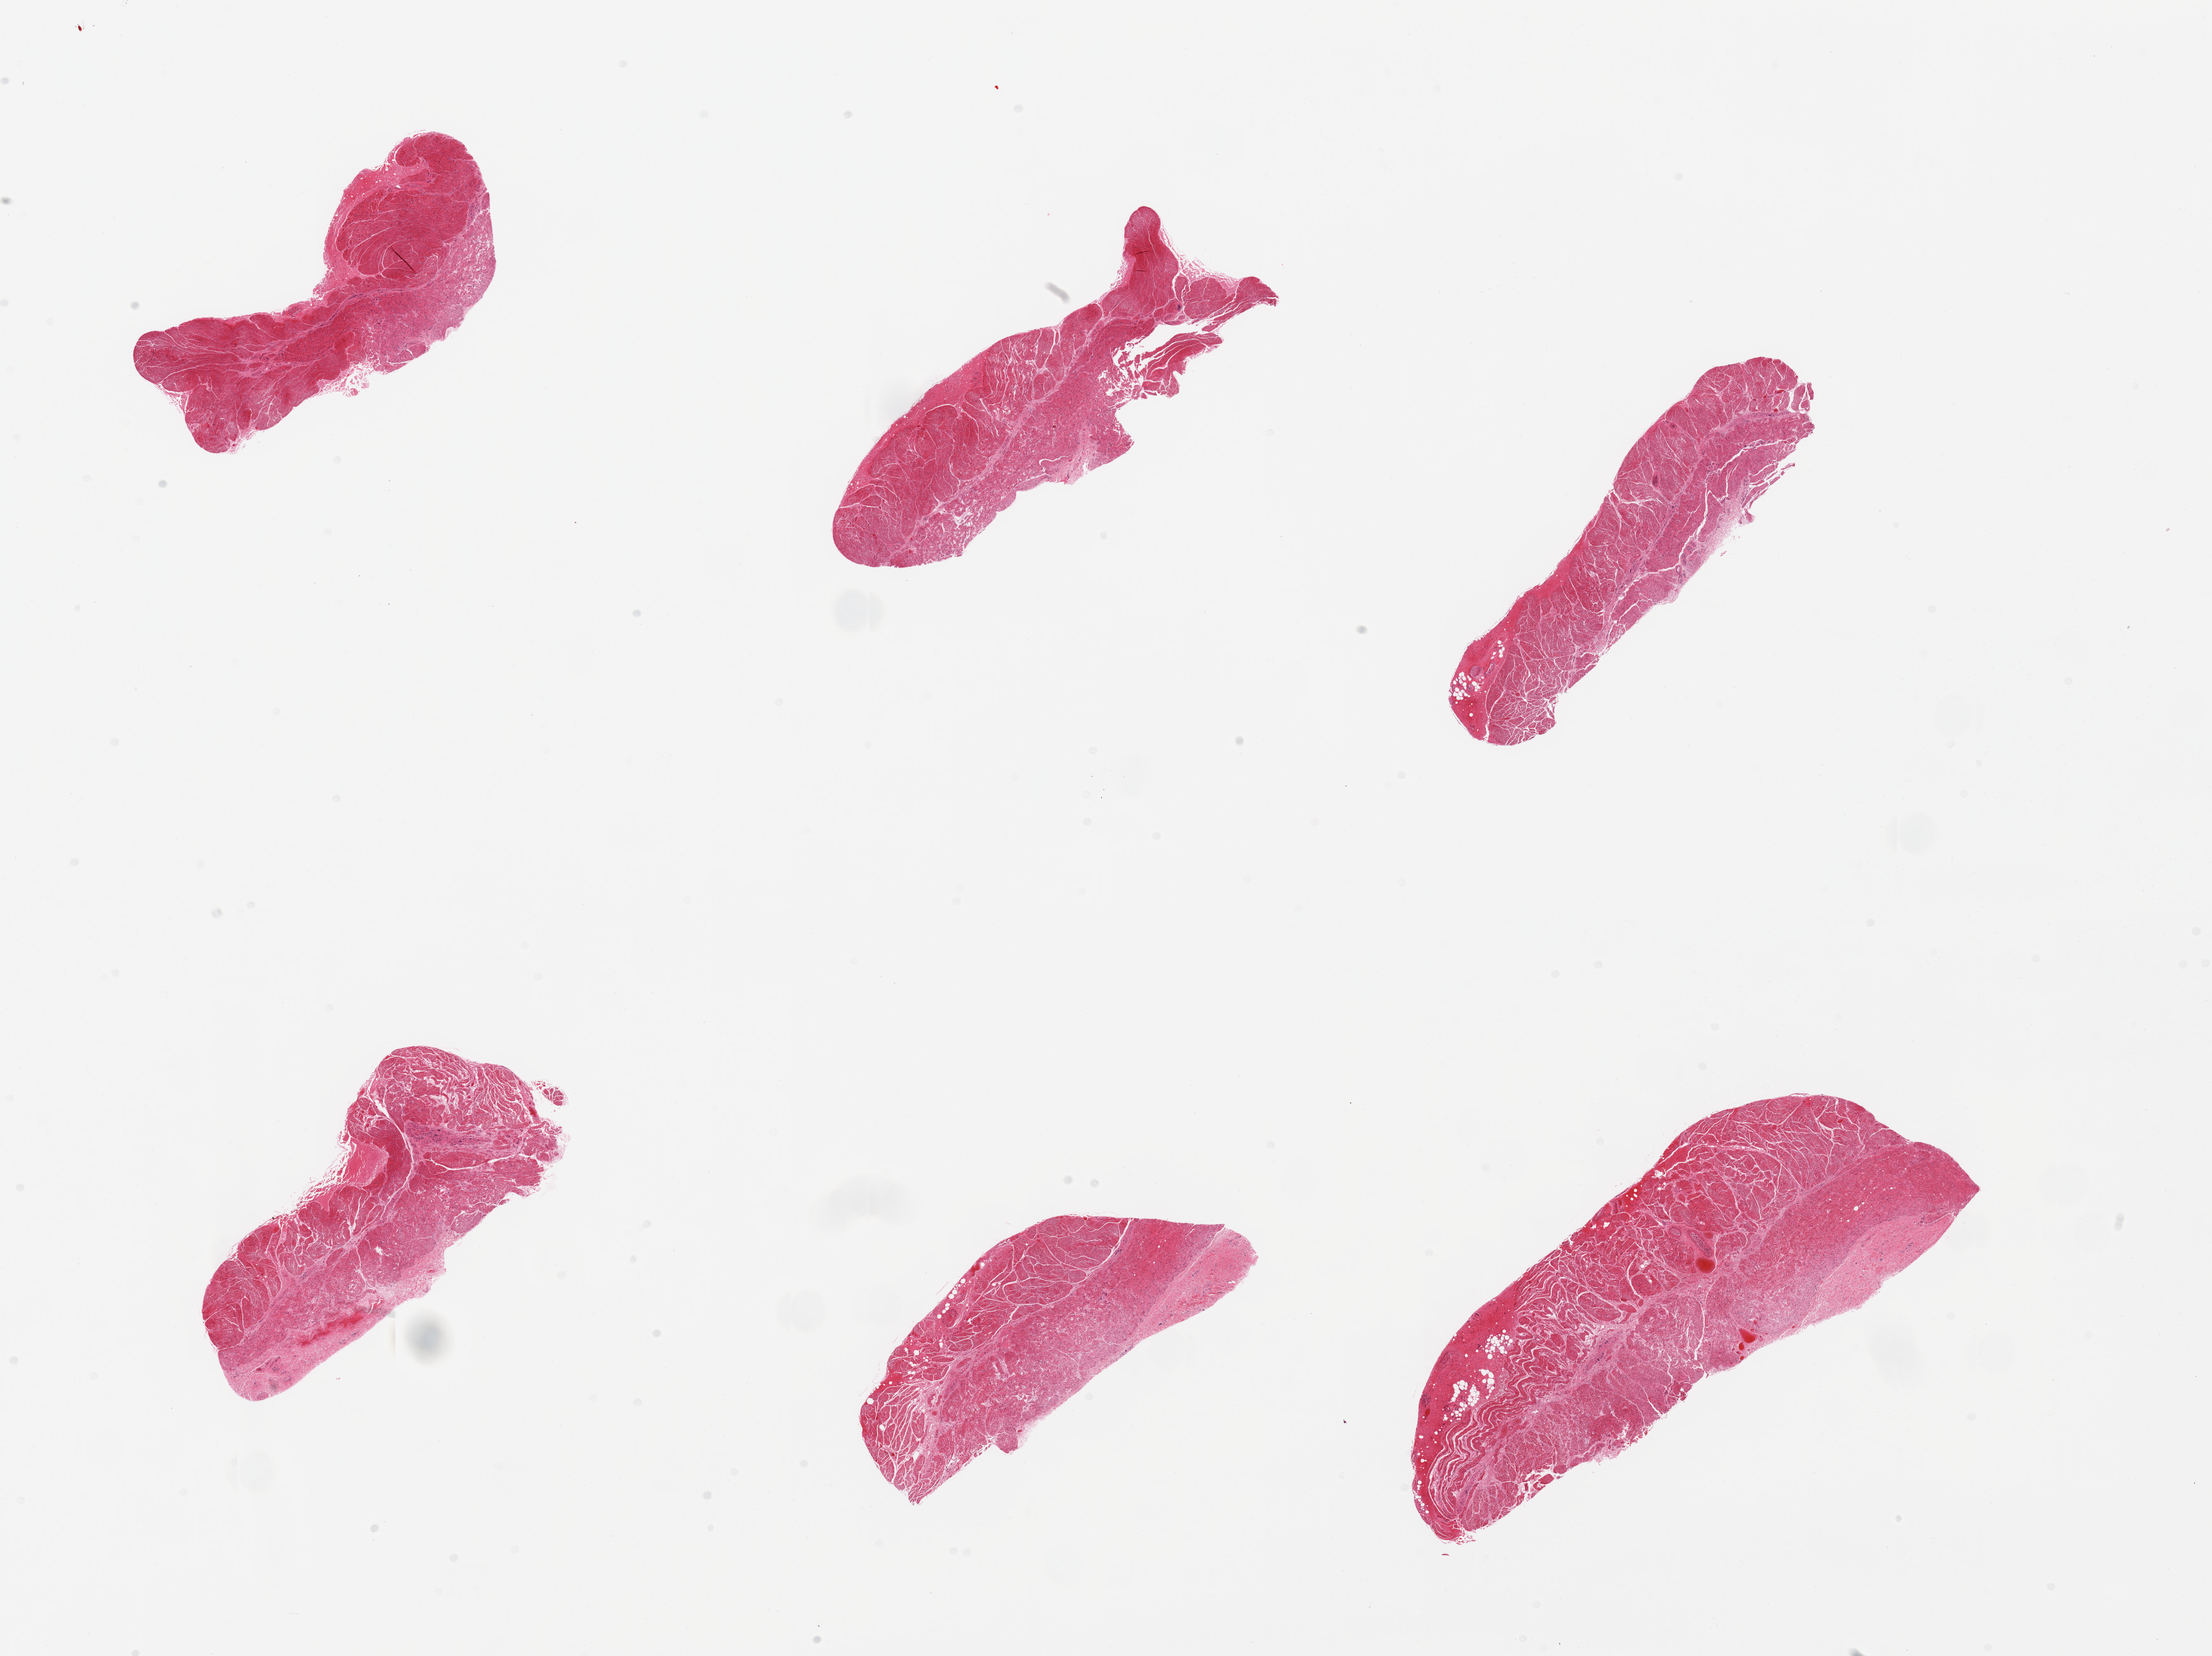
Digitized haematoxylin and eosin-stained section — shown as a low-resolution overview of the whole scanned area (about 27.6 x 20.6 mm), PAXgene-fixed paraffin-embedded (PFPE) section, section of esophageal muscle (target tissue), tissue donor sample.
• pathologist's review note for this sample: 6 pieces, all muscularis